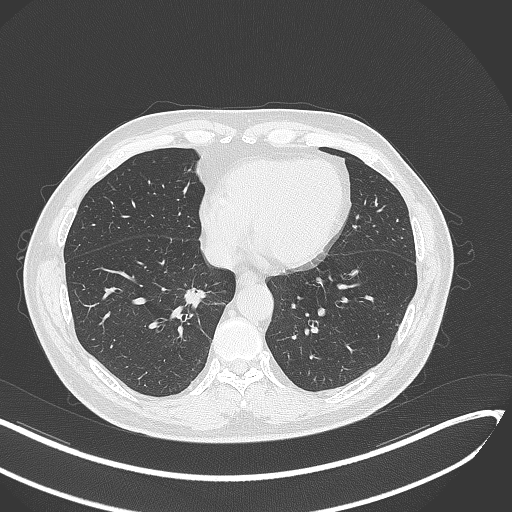
Chest CT, one axial slice. Position 129 of 429 along the scan axis. Reconstruction kernel B70f. Lung window (W 1500 / L -600 HU). 1 mm slice thickness. 512 × 512 image matrix, field of view 400 × 400 mm. Patient: male, 62 years. Case-level facts recorded for this patient, not image findings: clinical TNM (as recorded): T1b N0 M0; histopathological grade: G2.
Annotated regions visible in this slice (bounding box drawn by a radiologist):
- lung tumour (recorded histology: adenocarcinoma): bounding box (x1, y1, x2, y2) in pixels: (182, 286, 219, 314)